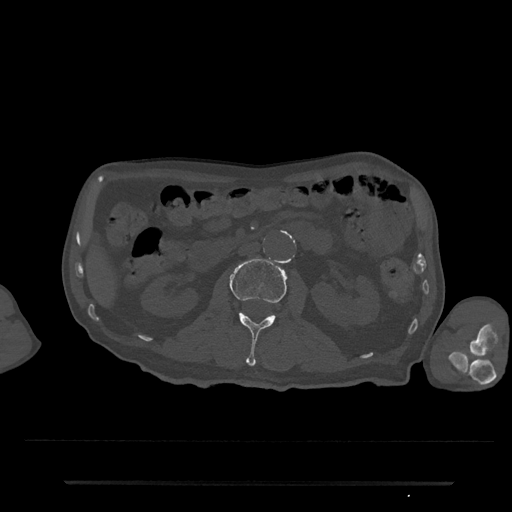
CT including the spine, one axial slice. Slice 49 of 797 in the series (ordered by position). Reconstruction kernel Br40s/3. 120 kVp. Bone window (W 1800 / L 400 HU). 0.5 mm slice thickness. 512 × 512 image matrix, field of view 427 × 427 mm. Patient: male, 74 years. Case-level facts recorded for this patient, not image findings: primary cancer: prostate.
Annotated regions visible in this slice (semi-automatically segmented with operator editing):
- L2 vertebra: bounding box <230,258,286,367> (left, top, right, bottom; pixels)